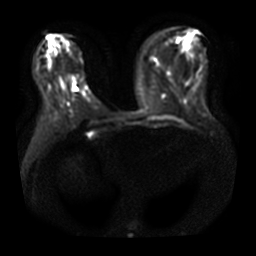
Breast MRI, one axial slice. Slice 14 of 38 in the series (ordered by position). Diffusion-weighted series; image 2 of 4 stored at this slice position (different b-values; order by instance number). 3 T. 5 mm slice thickness. 256 × 256 image matrix, field of view 360 × 360 mm. Female patient.
Outlined on this slice (outlined manually by an expert reader):
- tumour on diffusion-weighted imaging: bounding box [x1, y1, x2, y2] px = [72, 77, 75, 85]